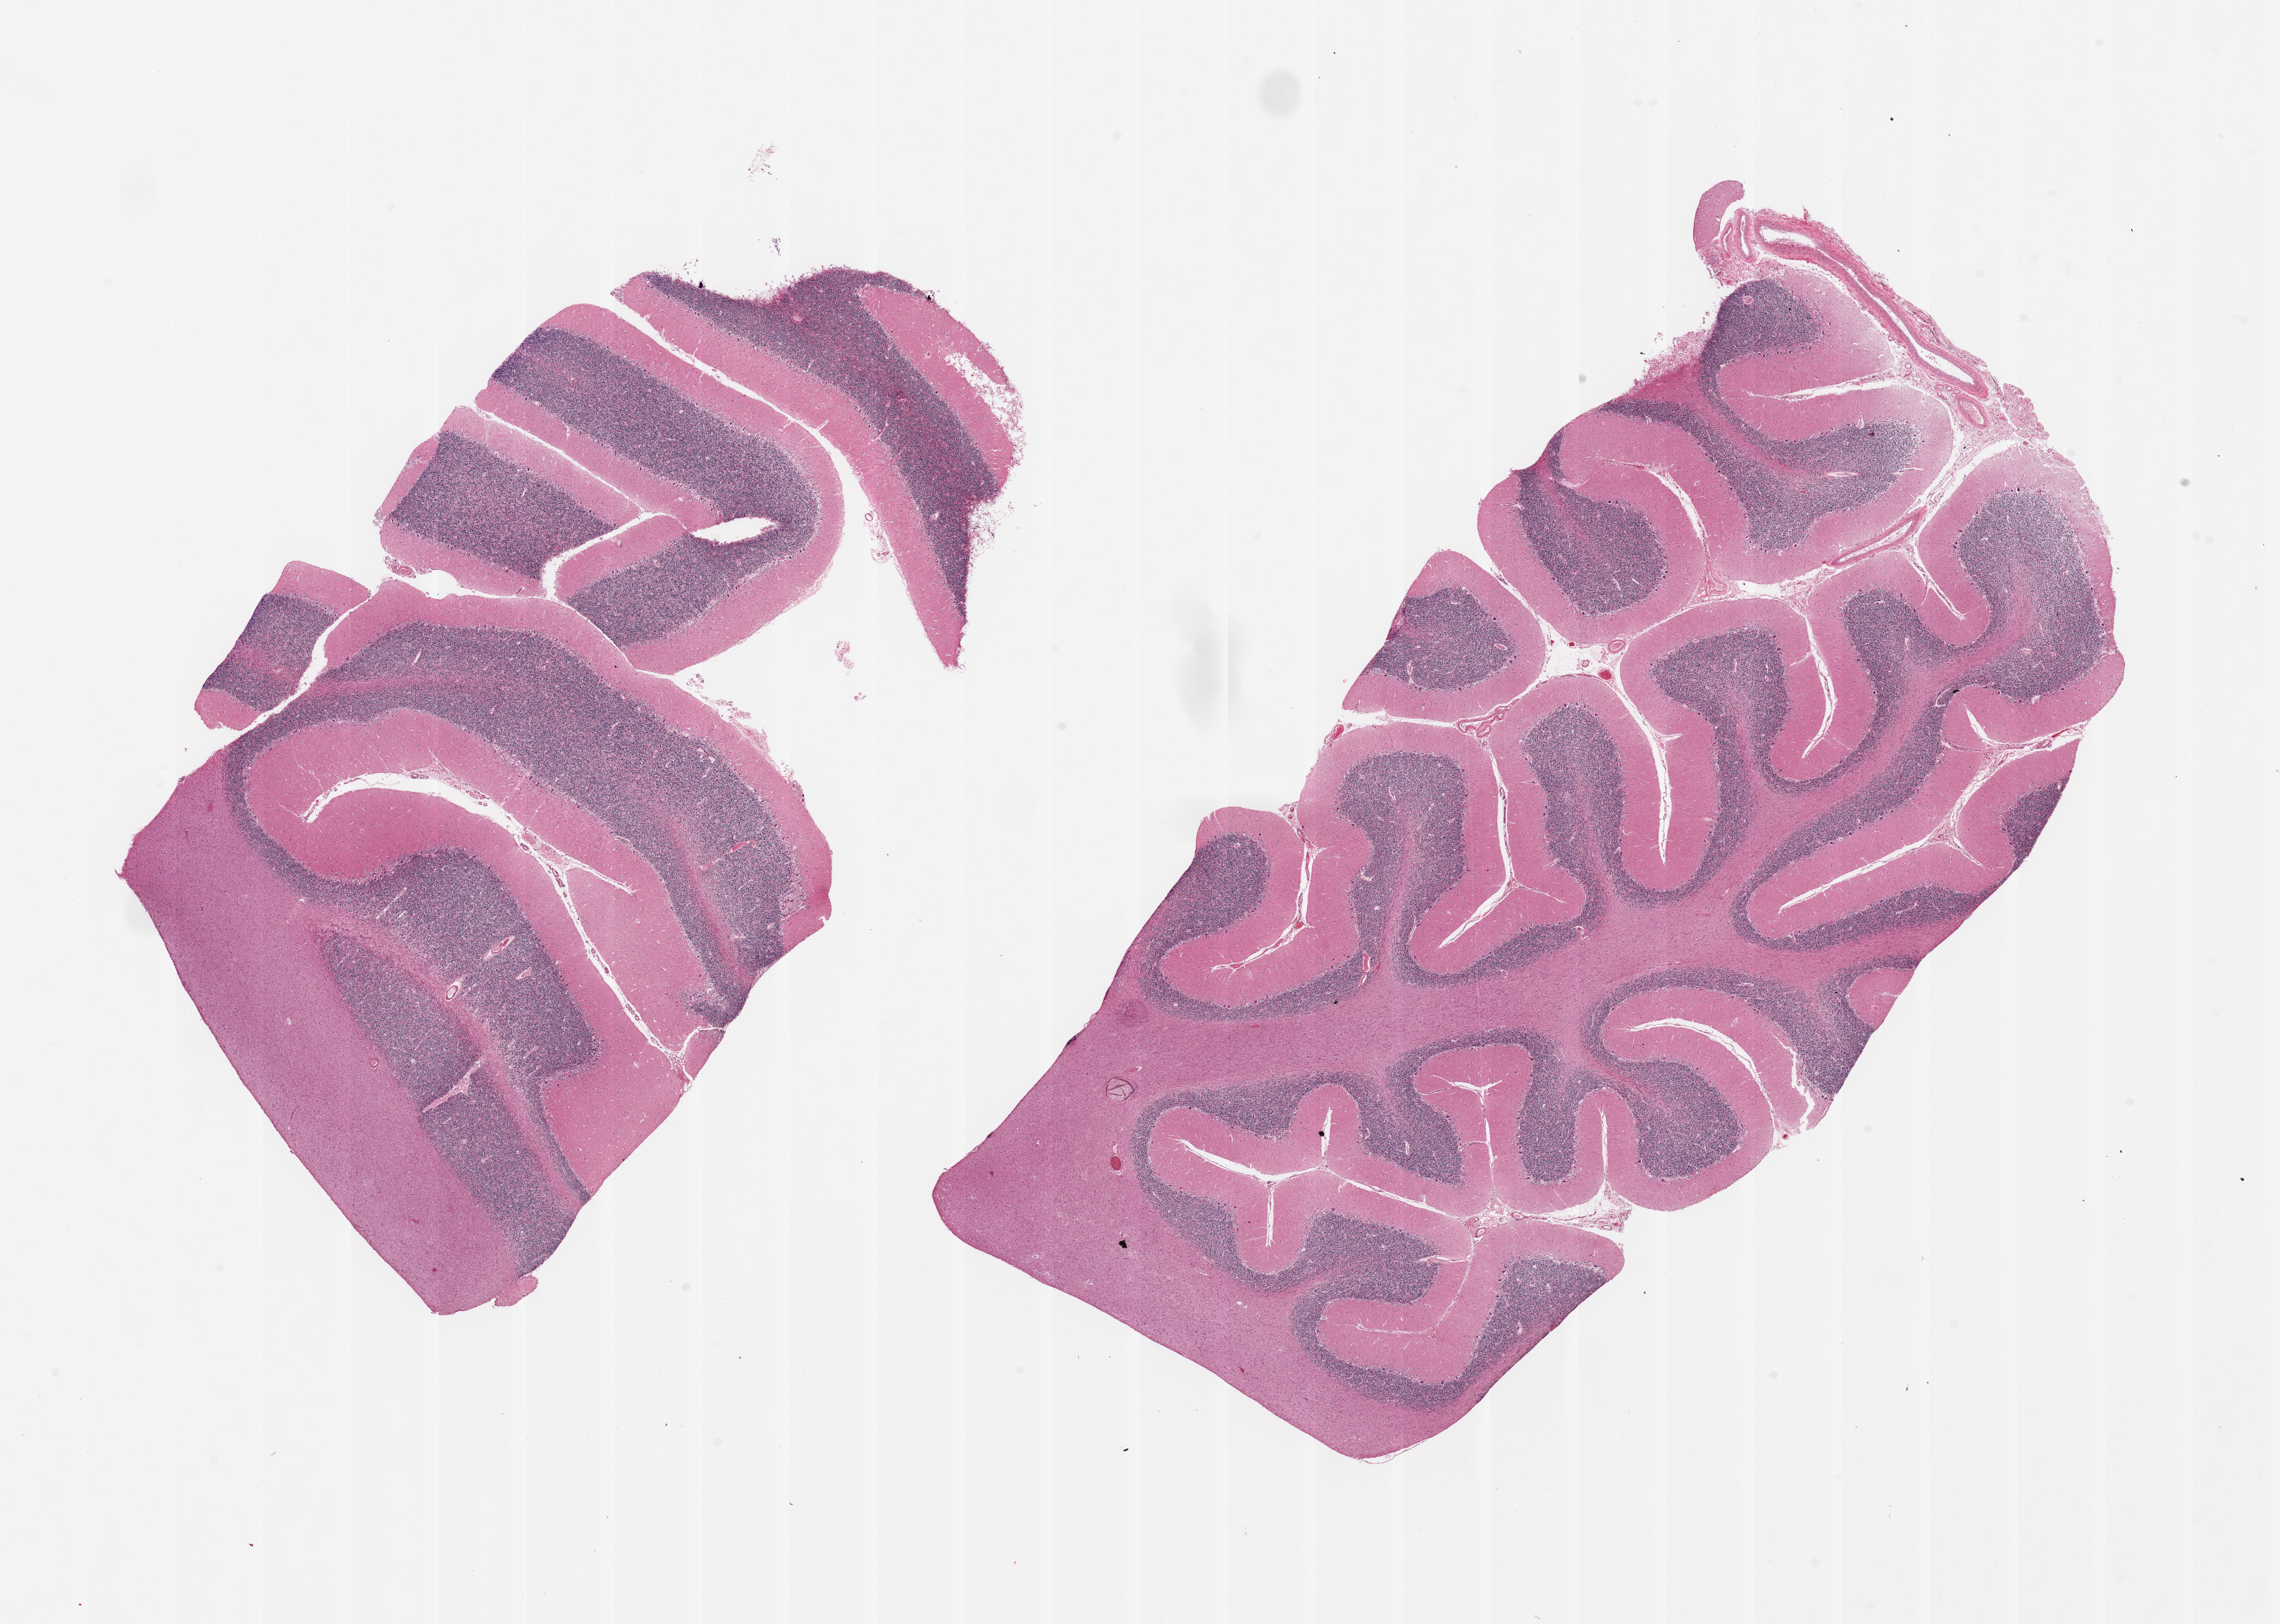
Digitized haematoxylin and eosin-stained section — whole scanned area (about 25.6 x 18.2 mm) shown as a low-resolution overview, PAXgene-fixed paraffin-embedded (PFPE) section, target tissue: cerebellum, tissue donor sample. Donor: male.
Review note (as recorded): 2 pieces; portion of attached meninges.